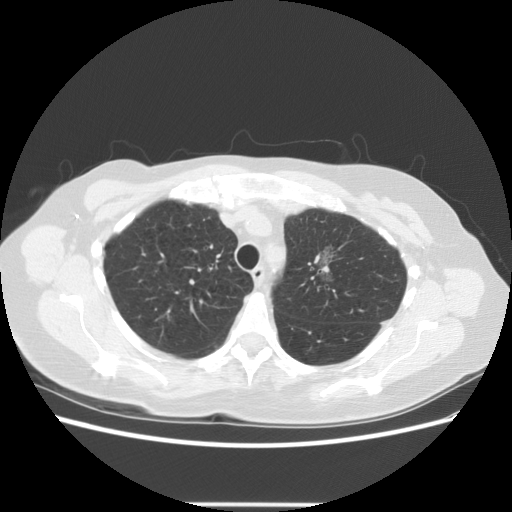
Low-dose screening chest CT, axial slice. Third annual screen. Lung window (W 1500 / L -600 HU). 2.5 mm slice thickness. Standard (soft-tissue) reconstruction kernel (STANDARD). Slice 97 of 126 in the series. 512 × 512 image matrix. Female, age 65 years at enrolment. Former smoker at enrolment.
• Expert reader's lesion annotation, box from (x=291, y=223) to (x=370, y=294) px.
• The exam's reader record, not a measurement of the box and not confirmed to be the same lesion: non-calcified nodule or mass ≥4 mm, left upper lobe, 17 × 14 mm, poorly defined margins, ground glass attenuation, pre-existing on the prior screen: yes; interval growth: yes.
• Participant outcome: lung cancer diagnosed 96 days after this screen — adenocarcinoma, NOS, left upper lobe, moderately differentiated (G2), stage IA (AJCC 6th edition), 30 mm at pathology.